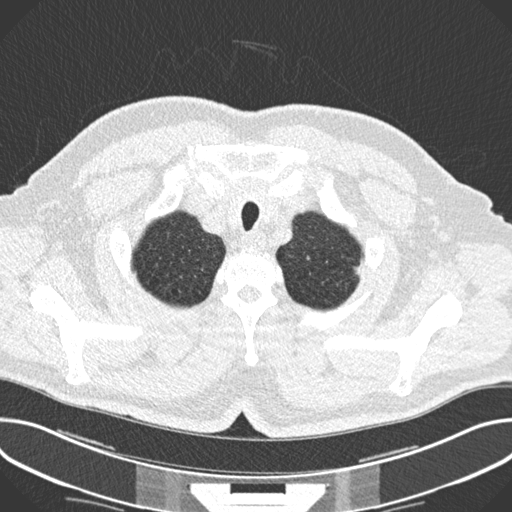
Low-dose screening chest CT, one axial slice; position 222 of 244 along the scan axis; 120 kVp; lung window (W 1500 / L -600 HU); 2 mm slice thickness; 512 × 512 image matrix.
Structures marked on this image (expert manual segmentation):
- lesion 1 (tumor, upper lobe of left lung): bounding box [x1, y1, x2, y2] px = [354, 267, 360, 276]